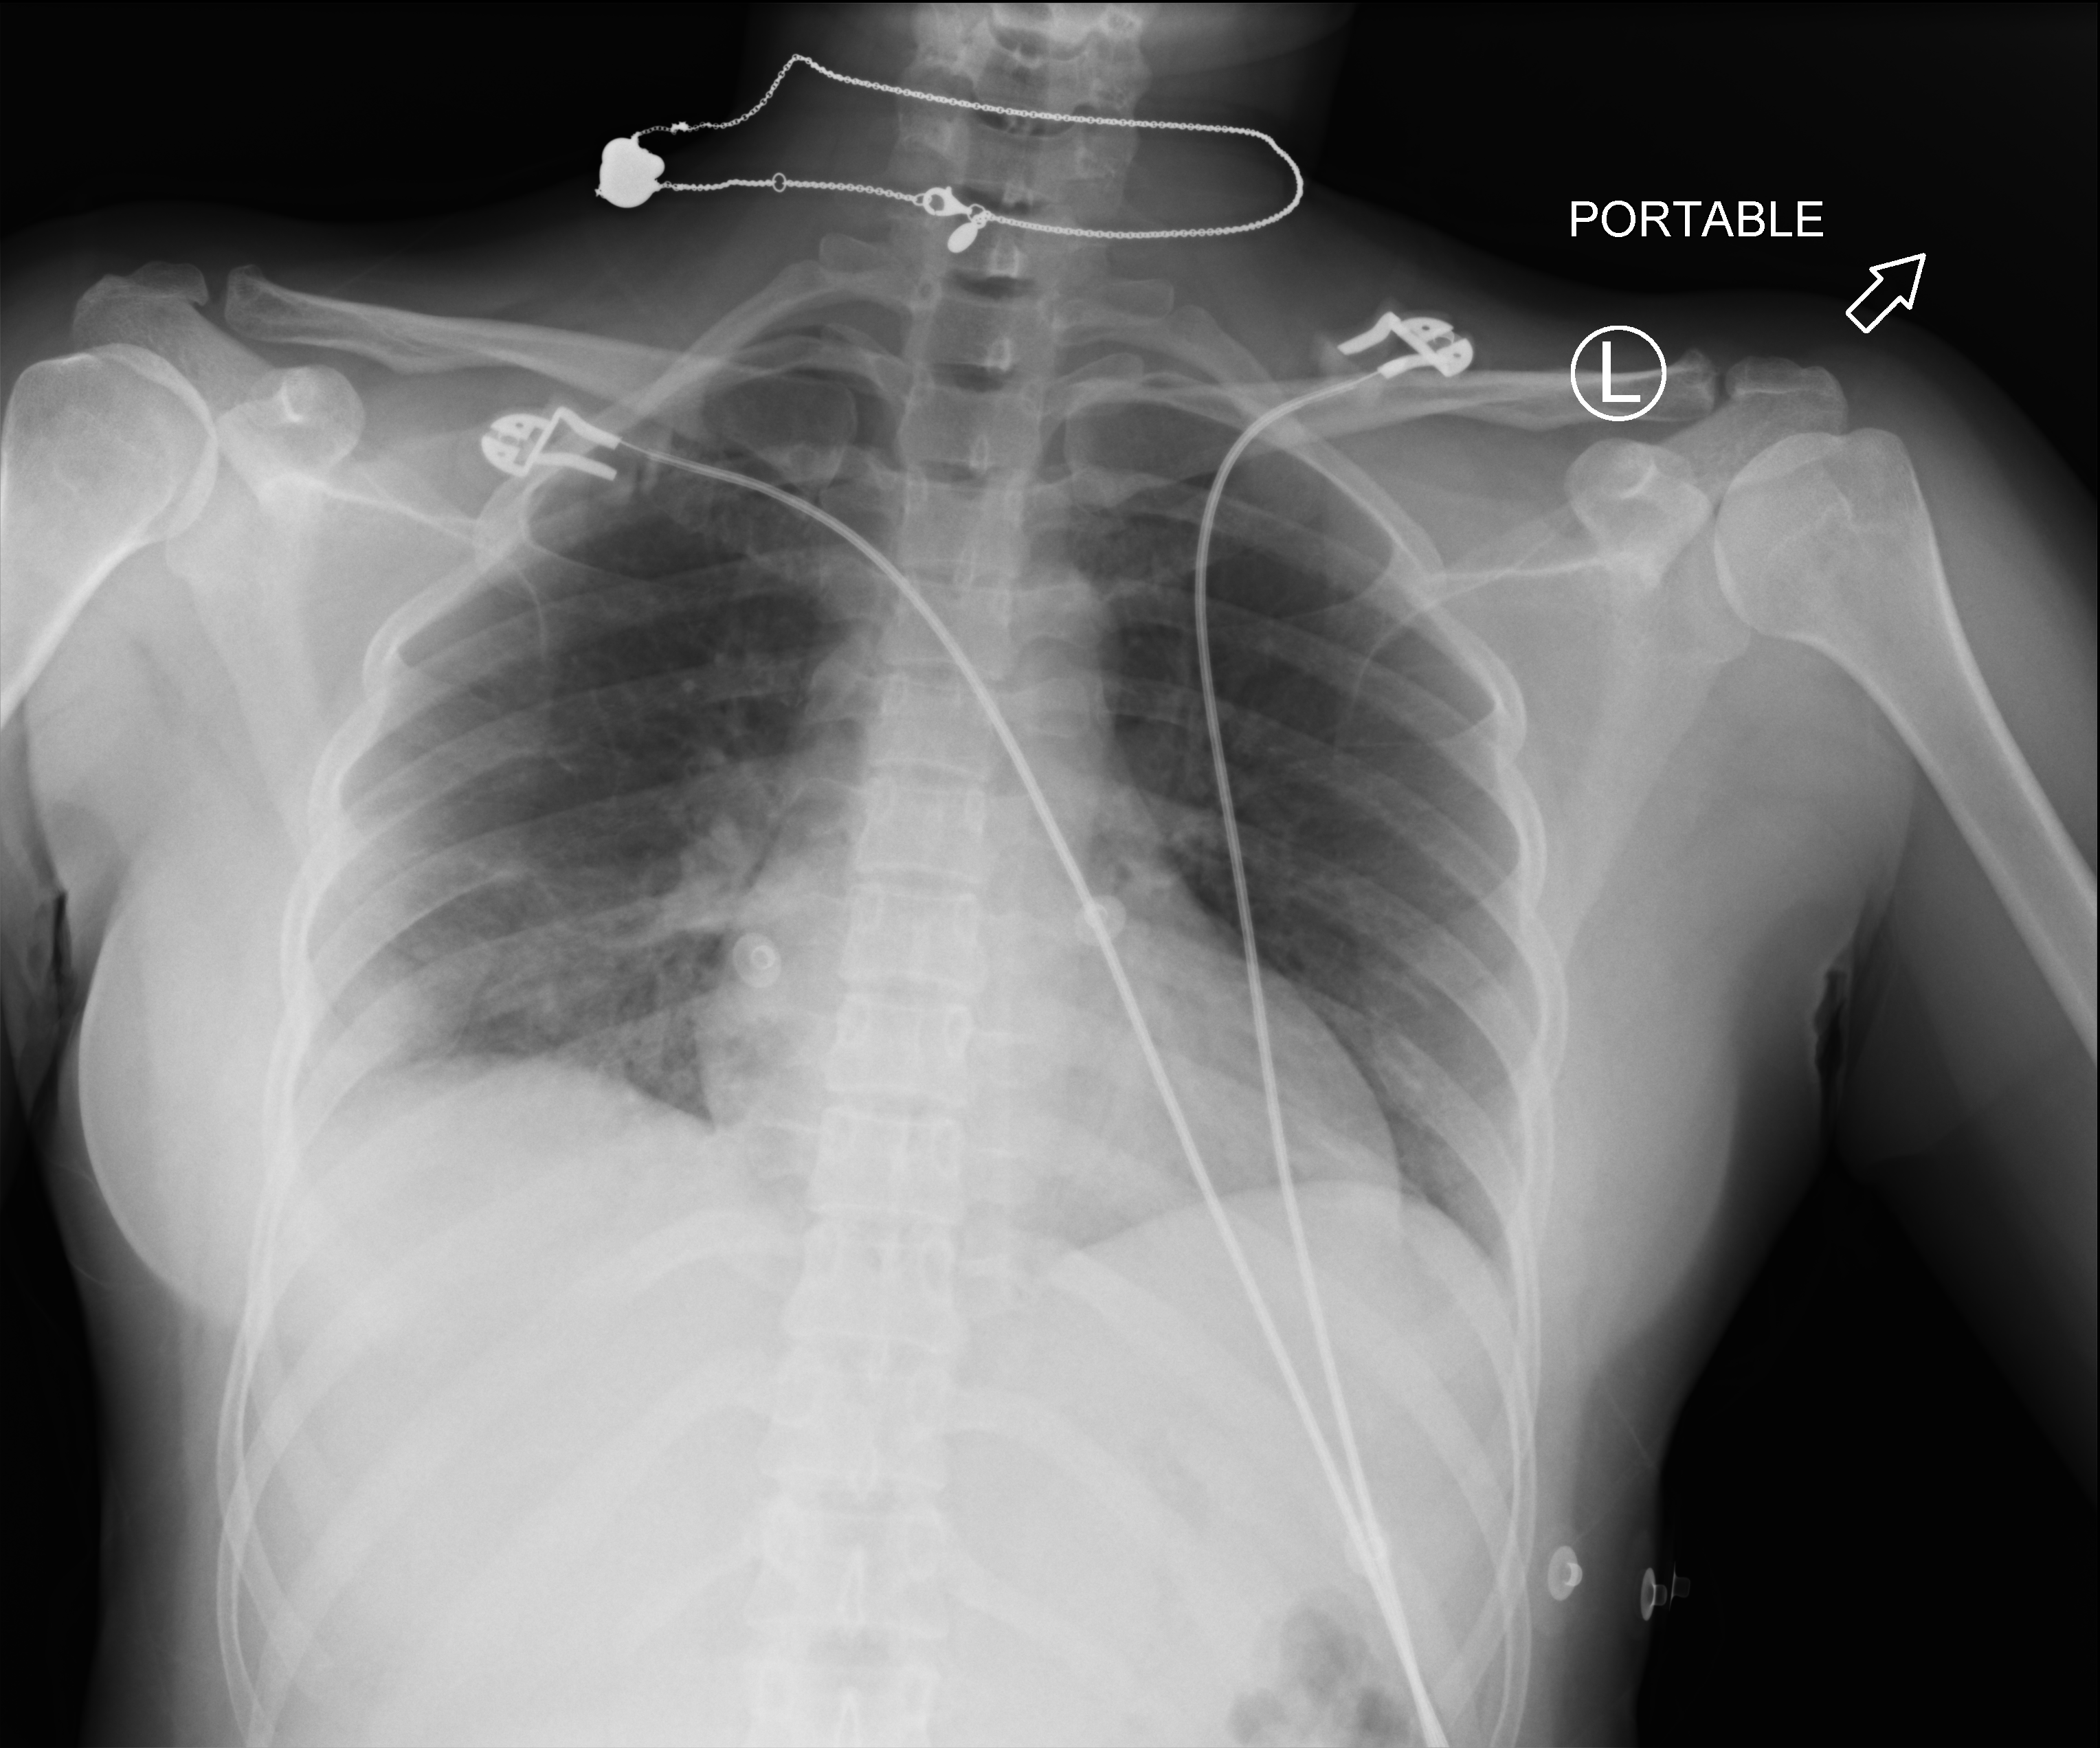
Chest X-ray (portable). Female patient hospitalised with COVID-19, age 18–59 years.
Admission-level facts for this patient (not findings on this image; timing relative to this image not recorded): mechanically ventilated during this hospital stay: no.